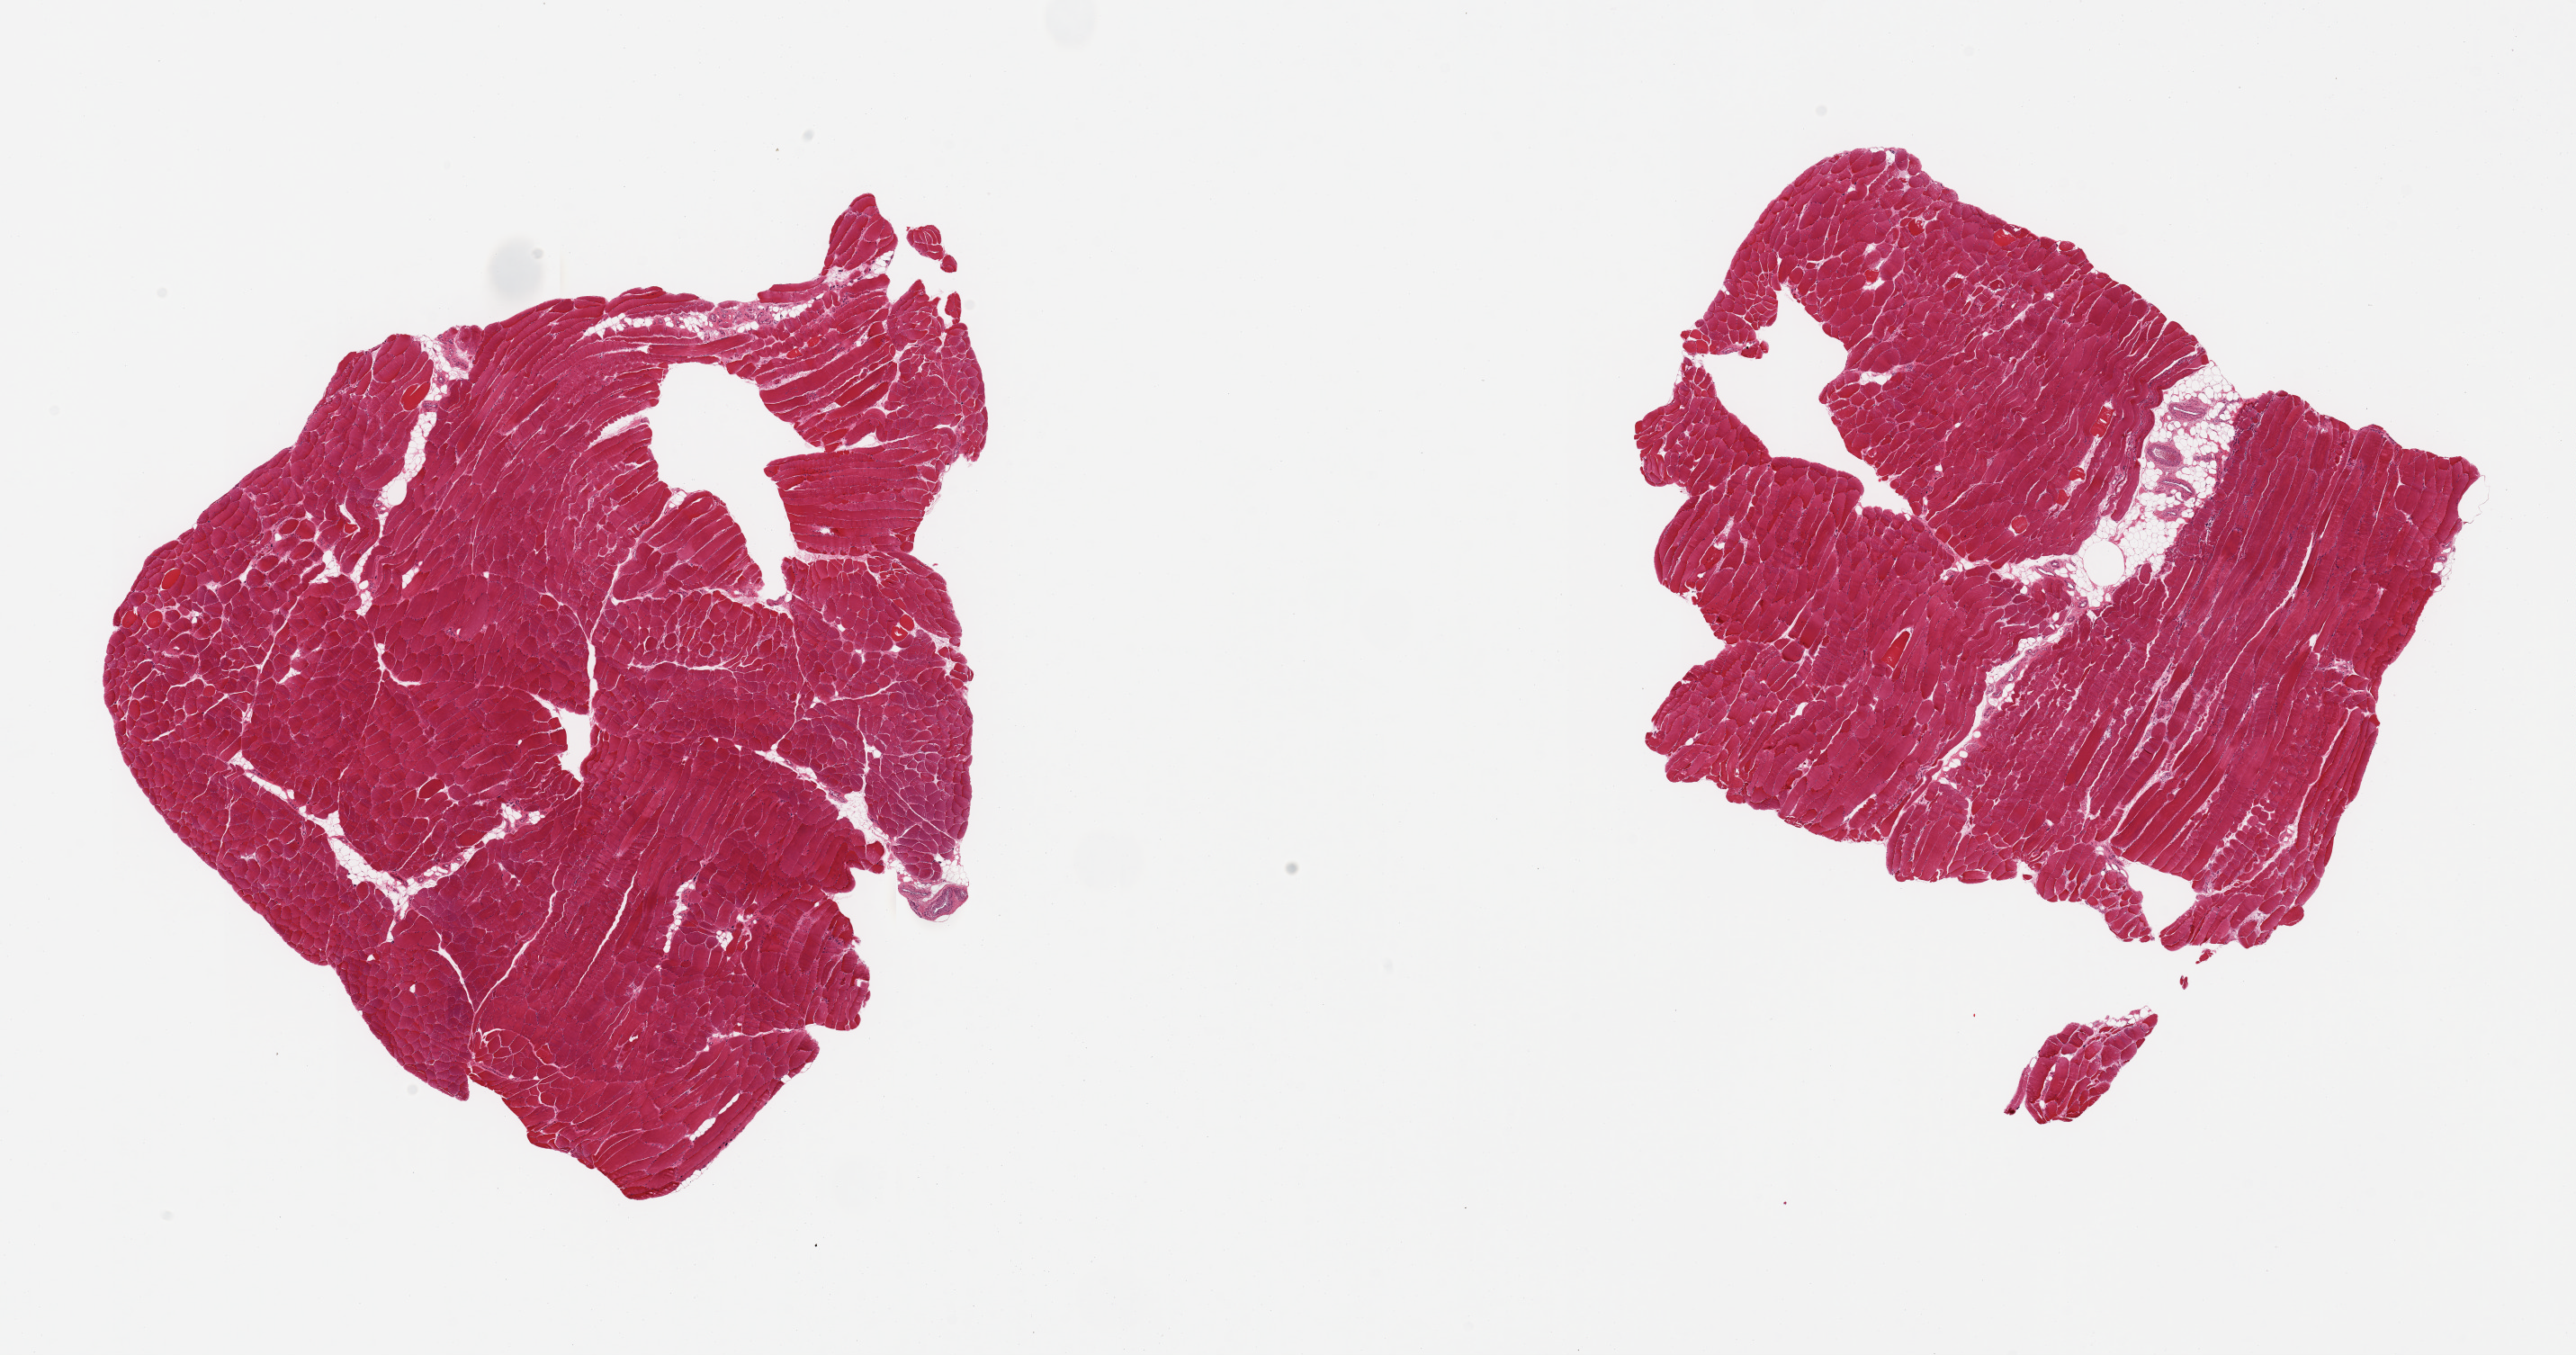
Haematoxylin and eosin whole-slide image — shown as a low-resolution overview of the whole scanned area (about 22.6 x 11.9 mm, acquisition: 20x scan), PAXgene-fixed paraffin-embedded (PFPE) section, section of skeletal muscle (target tissue), tissue donor sample.
Review note (as recorded): 2 pieces, interstitial fat/vascular elements are ~10%.